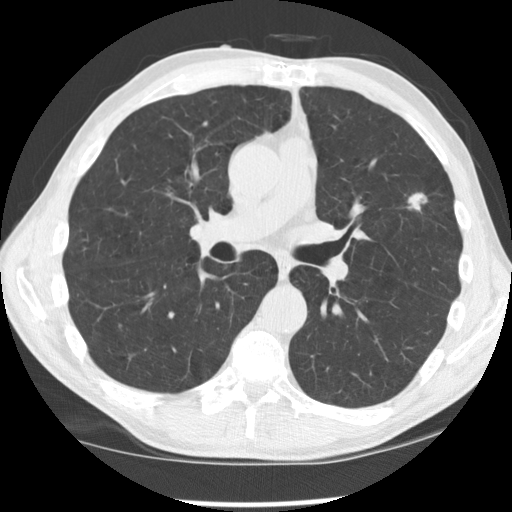
Low-dose screening chest CT, one axial slice. Slice 97 of 170 in the series (ordered by position). Lung window (W 1500 / L -600 HU). 2.5 mm slice thickness. 512 × 512 image matrix.
Outlined on this slice (expert manual segmentation):
- lesion 1 (tumor, upper lobe of left lung): bounding box (x1, y1, x2, y2) in pixels: (408, 193, 428, 212)